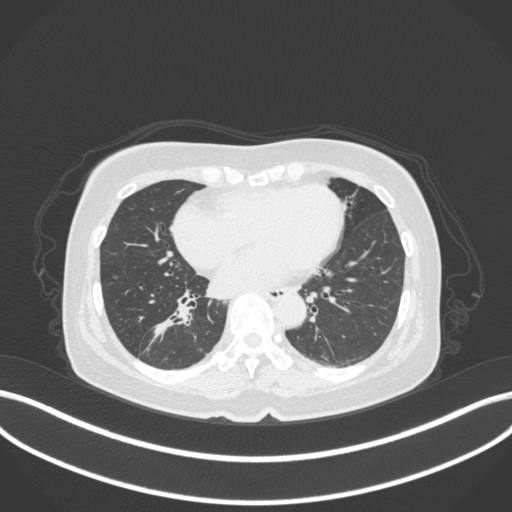
Chest CT, one axial slice. Slice 161 of 429 in the series (ordered by position). Lung window (W 1500 / L -600 HU). 1 mm slice thickness. 512 × 512 image matrix. Patient: female, 67 years. From the clinical record (not read from this slice): clinical TNM (as recorded): T1c N1 M0; histopathological grade: G2-3.
Outlined on this slice (bounding box drawn by a radiologist):
- lung tumour (recorded histology: adenocarcinoma): bounding box <149,308,178,337> (left, top, right, bottom; pixels)